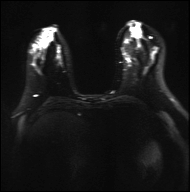
Breast MRI, one axial slice. Diffusion-weighted series; image 2 of 4 stored at this slice position (different b-values; order by instance number). 3 T. 190 × 192 image matrix. Female patient.
Structures marked on this image (outlined manually by an expert reader):
- tumour on diffusion-weighted imaging: box from (x=66, y=27) to (x=85, y=36) px